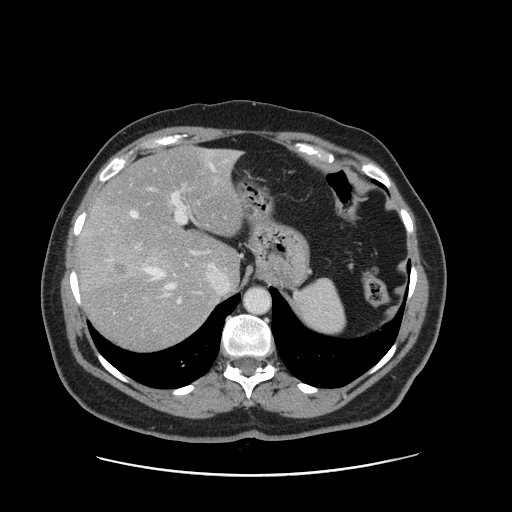
Contrast-enhanced abdominal CT, one axial slice. 120 kVp. Intravenous contrast given. Soft-tissue window (W 400 / L 40 HU). 2.5 mm slice thickness. 512 × 512 image matrix, field of view 398 × 398 mm. Female patient, age 62 years. From the clinical record (not read from this slice): diagnosis: colorectal cancer liver metastases, imaged before liver resection; multiple liver metastases: no; largest metastasis: 2.5 cm; disease in both lobes: no.
Annotated regions visible in this slice (manually delineated by an expert):
- hepatic veins: box from (x=131, y=153) to (x=239, y=291) px
- liver: (x=80, y=148)–(x=242, y=352)
- planned liver remnant (the part of the liver to remain after resection): (x=98, y=148)–(x=241, y=280)
- portal vein (with intrahepatic branches): (x=125, y=185)–(x=190, y=303)
- liver metastasis: (x=112, y=262)–(x=127, y=276)